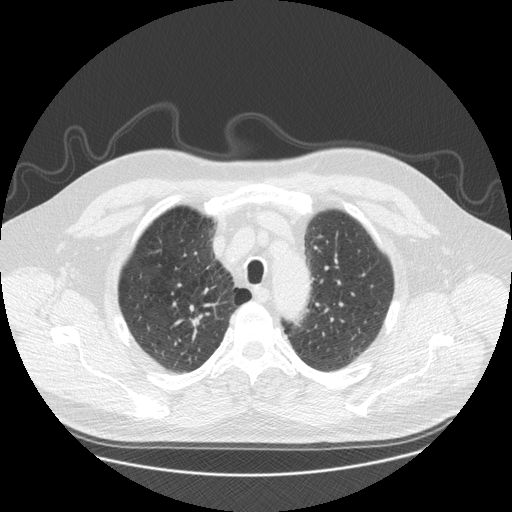
Low-dose screening chest CT, one axial slice; slice 142 of 173 in the series (ordered by position); reconstruction kernel STANDARD; 120 kVp; lung window (W 1500 / L -600 HU); 2.5 mm slice thickness; 512 × 512 image matrix, field of view 400 × 400 mm.
Annotated regions visible in this slice (expert manual segmentation):
- lesion 1 (tumor, upper lobe of right lung): bounding box <192,315,202,331> (left, top, right, bottom; pixels)